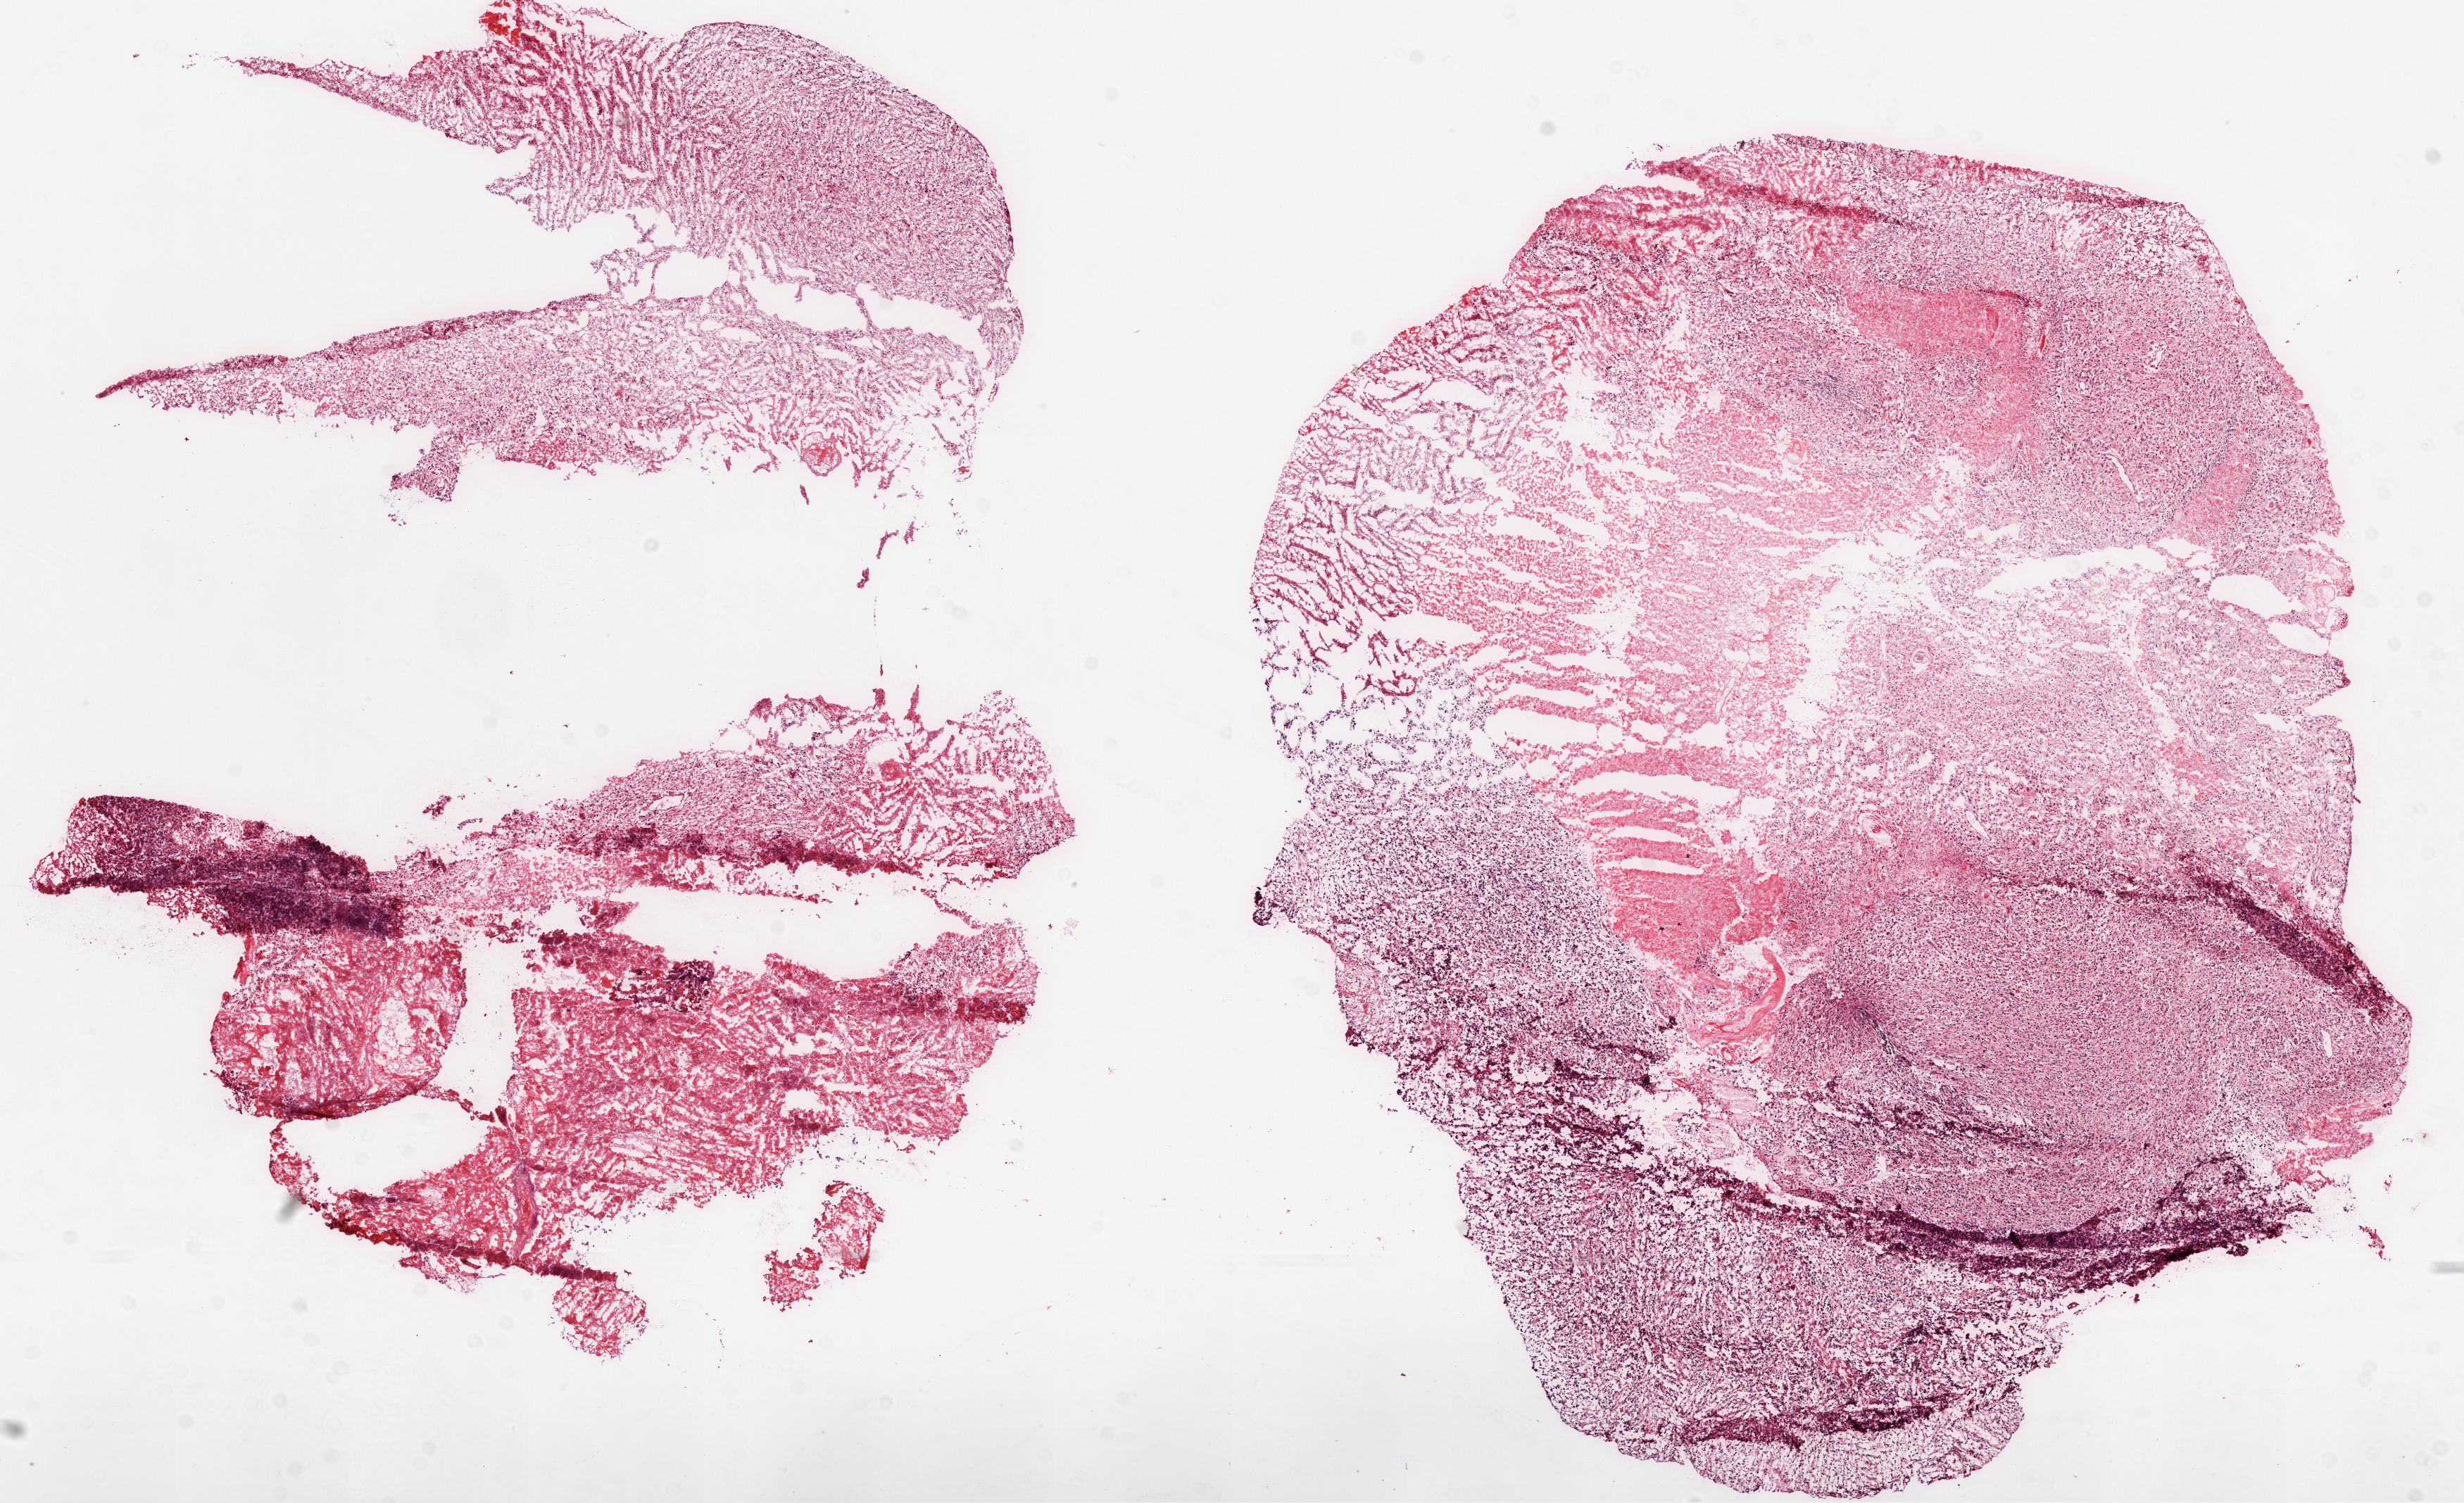
Digitized Hematoxylin and eosin (H&E) stained tissue section (whole slide), whole scanned area (about 14.0 x 8.6 mm) shown as a low-resolution overview. Frozen section. Primary tumour sample from the brain. Female, age 63 years at initial diagnosis. Composition of this section per pathologist review: tumour cells 60%, tumour nuclei 100%, normal cells 0%, stromal cells 0%, necrosis 40%.
Histologic diagnosis: Glioblastoma.